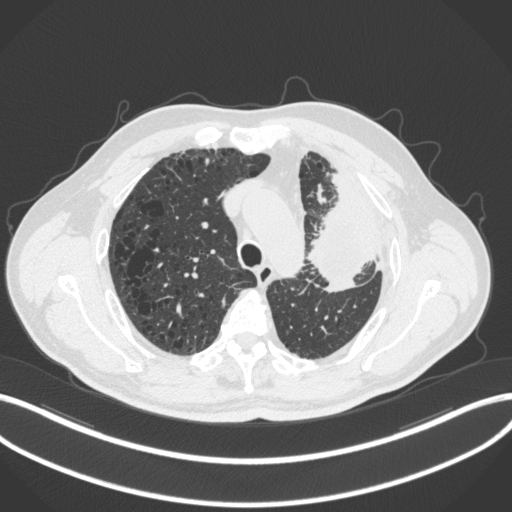
Chest CT, one axial slice; position 226 of 286 along the scan axis; reconstruction kernel B31f; 120 kVp; lung window (W 1500 / L -600 HU); 1 mm slice thickness; 512 × 512 image matrix, field of view 400 × 400 mm. Patient: male, 68 years. Case-level facts recorded for this patient, not image findings: clinical TNM (as recorded): T3 N3 M1.
Annotated regions visible in this slice (rectangle marked by the reading radiologist):
- lung tumour (recorded histology: adenocarcinoma): box from (x=301, y=183) to (x=380, y=291) px